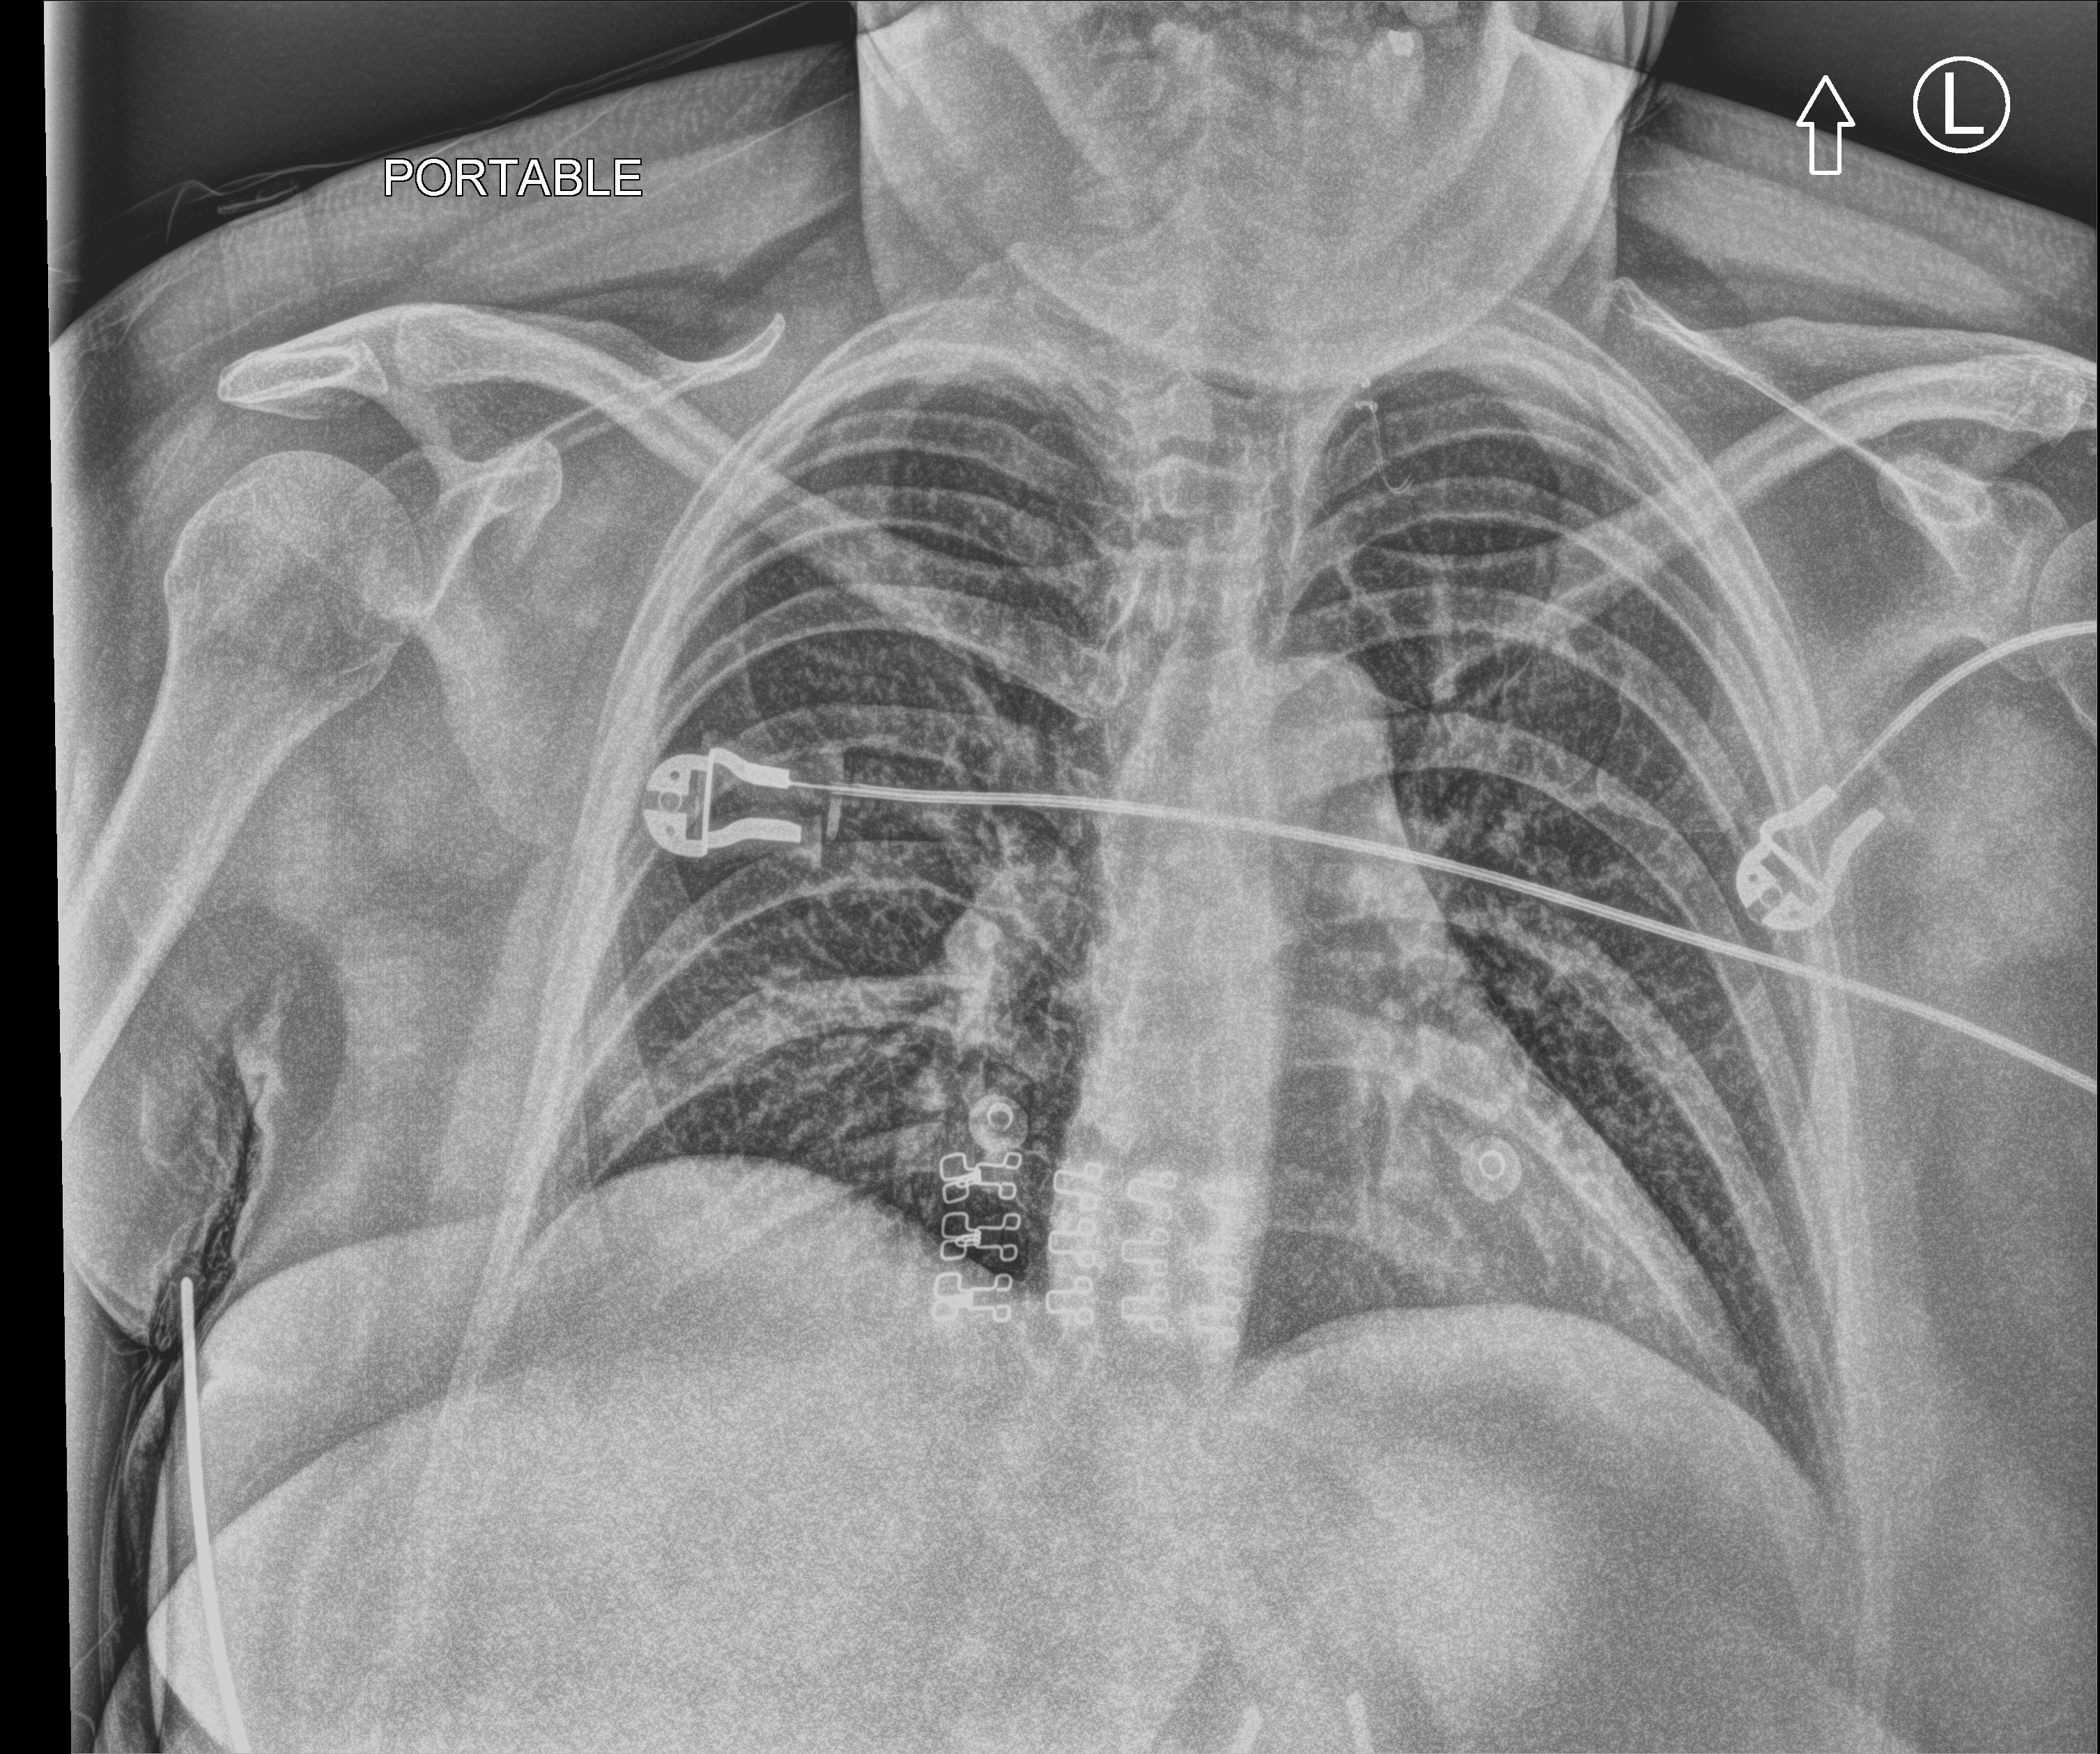
Chest X-ray (portable). Female patient hospitalised with COVID-19, age 18–59 years.
Hospital-stay facts (about this admission, not read from this image; timing relative to this image not recorded):
- mechanically ventilated during this hospital stay: no